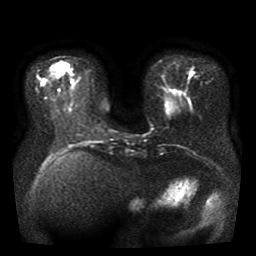
Breast MRI, one axial slice; slice 13 of 41 in the series (ordered by position); diffusion-weighted series; image 2 of 4 stored at this slice position (different b-values; order by instance number); 1.5 T; 5 mm slice thickness; 256 × 256 image matrix, field of view 330 × 330 mm. Female patient.
Outlined on this slice (expert manual segmentation):
- tumour on diffusion-weighted imaging: bounding box <190,71,194,75> (left, top, right, bottom; pixels)